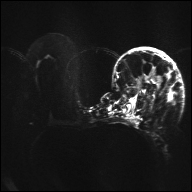
Breast MRI, one axial slice; slice 18 of 32 in the series (ordered by position); diffusion-weighted series; image 2 of 4 stored at this slice position (different b-values; order by instance number); 1.5 T; 4 mm slice thickness; 192 × 192 image matrix, field of view 360 × 360 mm. Female patient.
Outlined on this slice (manually delineated by an expert):
- tumour on diffusion-weighted imaging: bounding box [x1, y1, x2, y2] px = [152, 70, 161, 81]